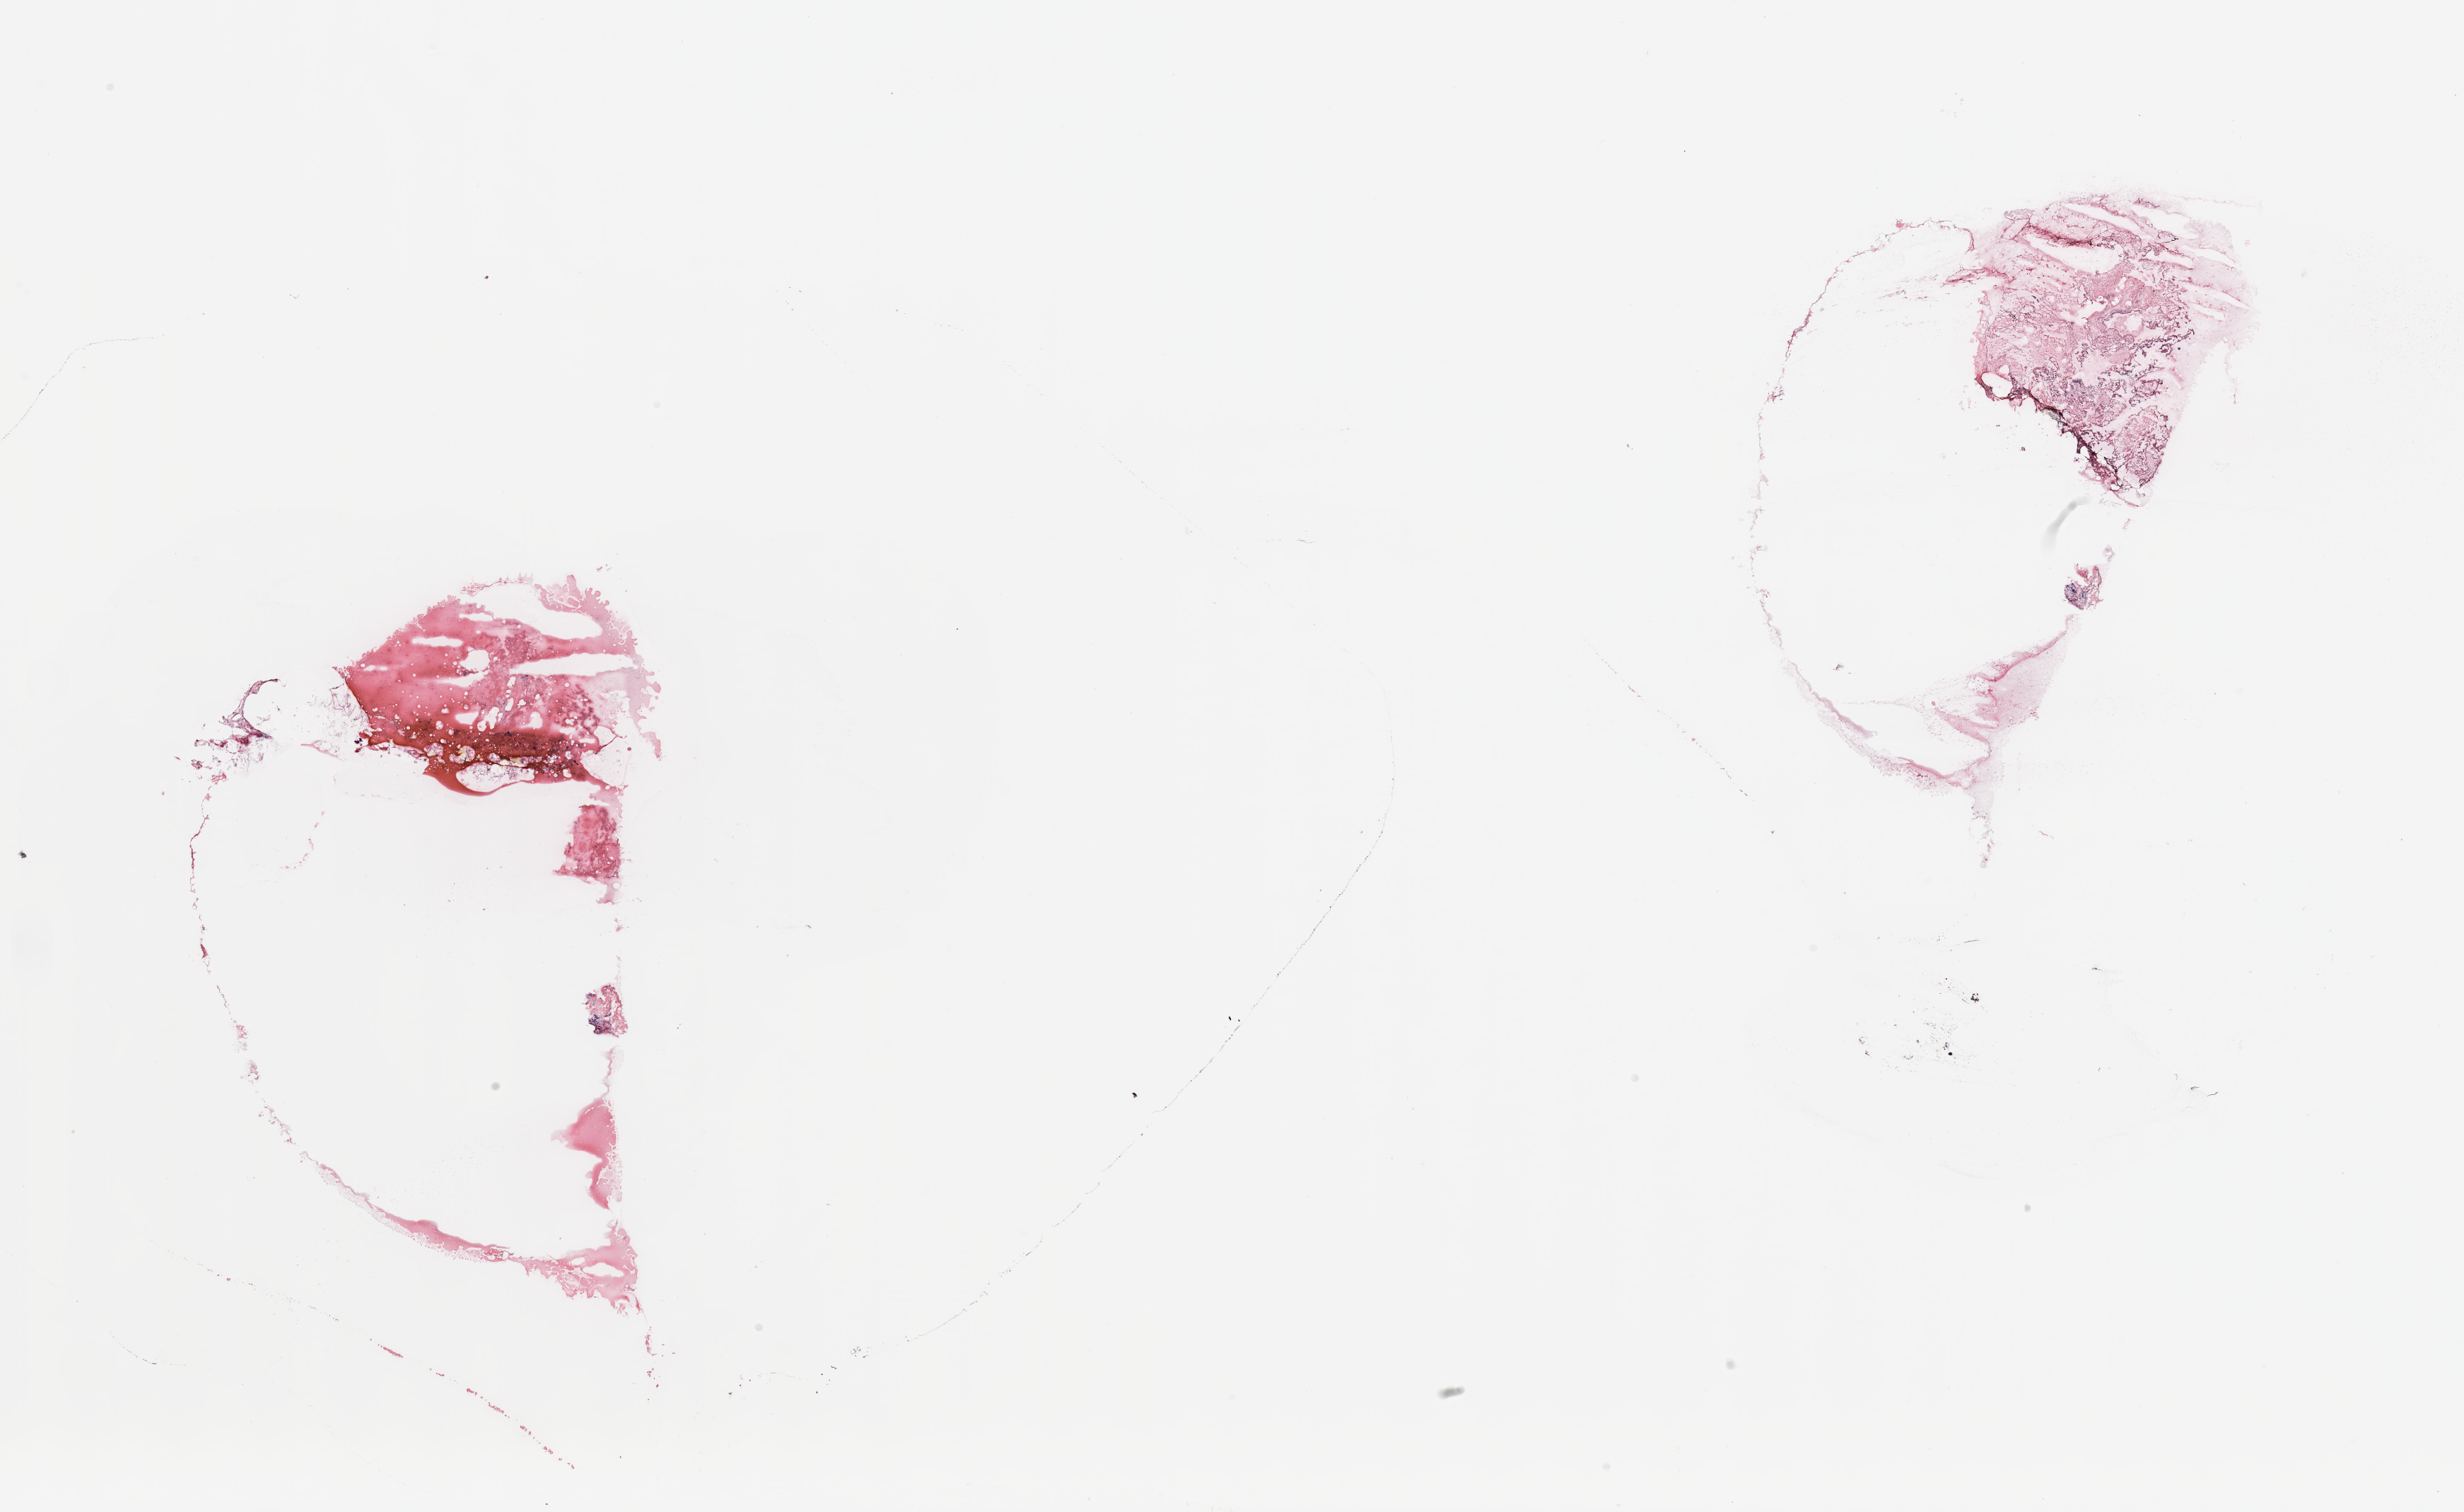
Hematoxylin and eosin (H&E) stained whole-slide image, whole scanned area (about 27.6 x 16.9 mm) shown as a low-resolution overview; breast, tissue type not recorded.
Patient diagnosis (cohort enrolment): breast cancer (breast).